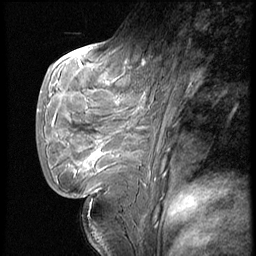
Breast MRI (dynamic contrast-enhanced), one sagittal slice. Position 22 of 62 along the scan axis. Dynamic contrast-enhanced series, image 2 of 4 at this slice position (ordered by acquisition). 1.5 T. TE 4.2 ms, TR 9 ms. 2.5 mm slice thickness. 256 × 256 image matrix, field of view 180 × 180 mm. Female patient, age 28 years. Case-level facts recorded for this patient, not image findings: setting: breast cancer imaged before/during neoadjuvant chemotherapy.
Annotated regions visible in this slice (semi-automatically segmented with operator editing):
- analysis volume of interest (the breast-tissue region the enhancement analysis was run in; not a lesion): bounding box (x1, y1, x2, y2) in pixels: (43, 54, 150, 183)
- tumour enhancement mask (voxels above the 140 % enhancement threshold inside the analysis volume of interest): (80, 62, 145, 171)